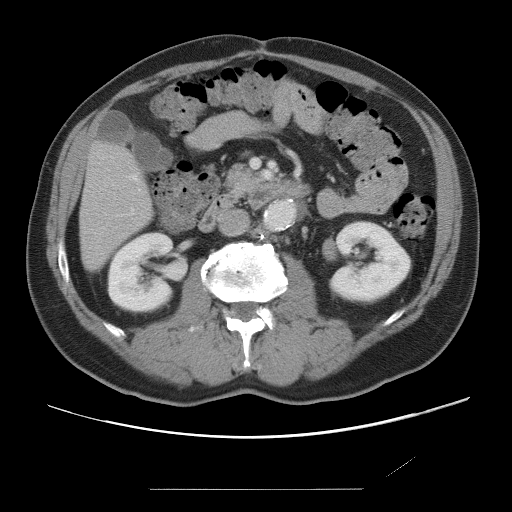
Contrast-enhanced abdominal CT, one axial slice. 120 kVp. Soft-tissue window (W 400 / L 40 HU). 5 mm slice thickness. 512 × 512 image matrix, field of view 406 × 406 mm. Male patient, age 74 years. Case-level facts recorded for this patient, not image findings: diagnosis: colorectal cancer liver metastases, imaged before liver resection; multiple liver metastases: yes; largest metastasis: 1.1 cm; disease in both lobes: no.
Structures marked on this image (manually delineated by an expert):
- hepatic veins: bounding box <132,175,137,180> (left, top, right, bottom; pixels)
- liver: <80,144,150,270>
- planned liver remnant (the part of the liver to remain after resection): <80,144,150,270>
- portal vein (with intrahepatic branches): <132,209,134,214>